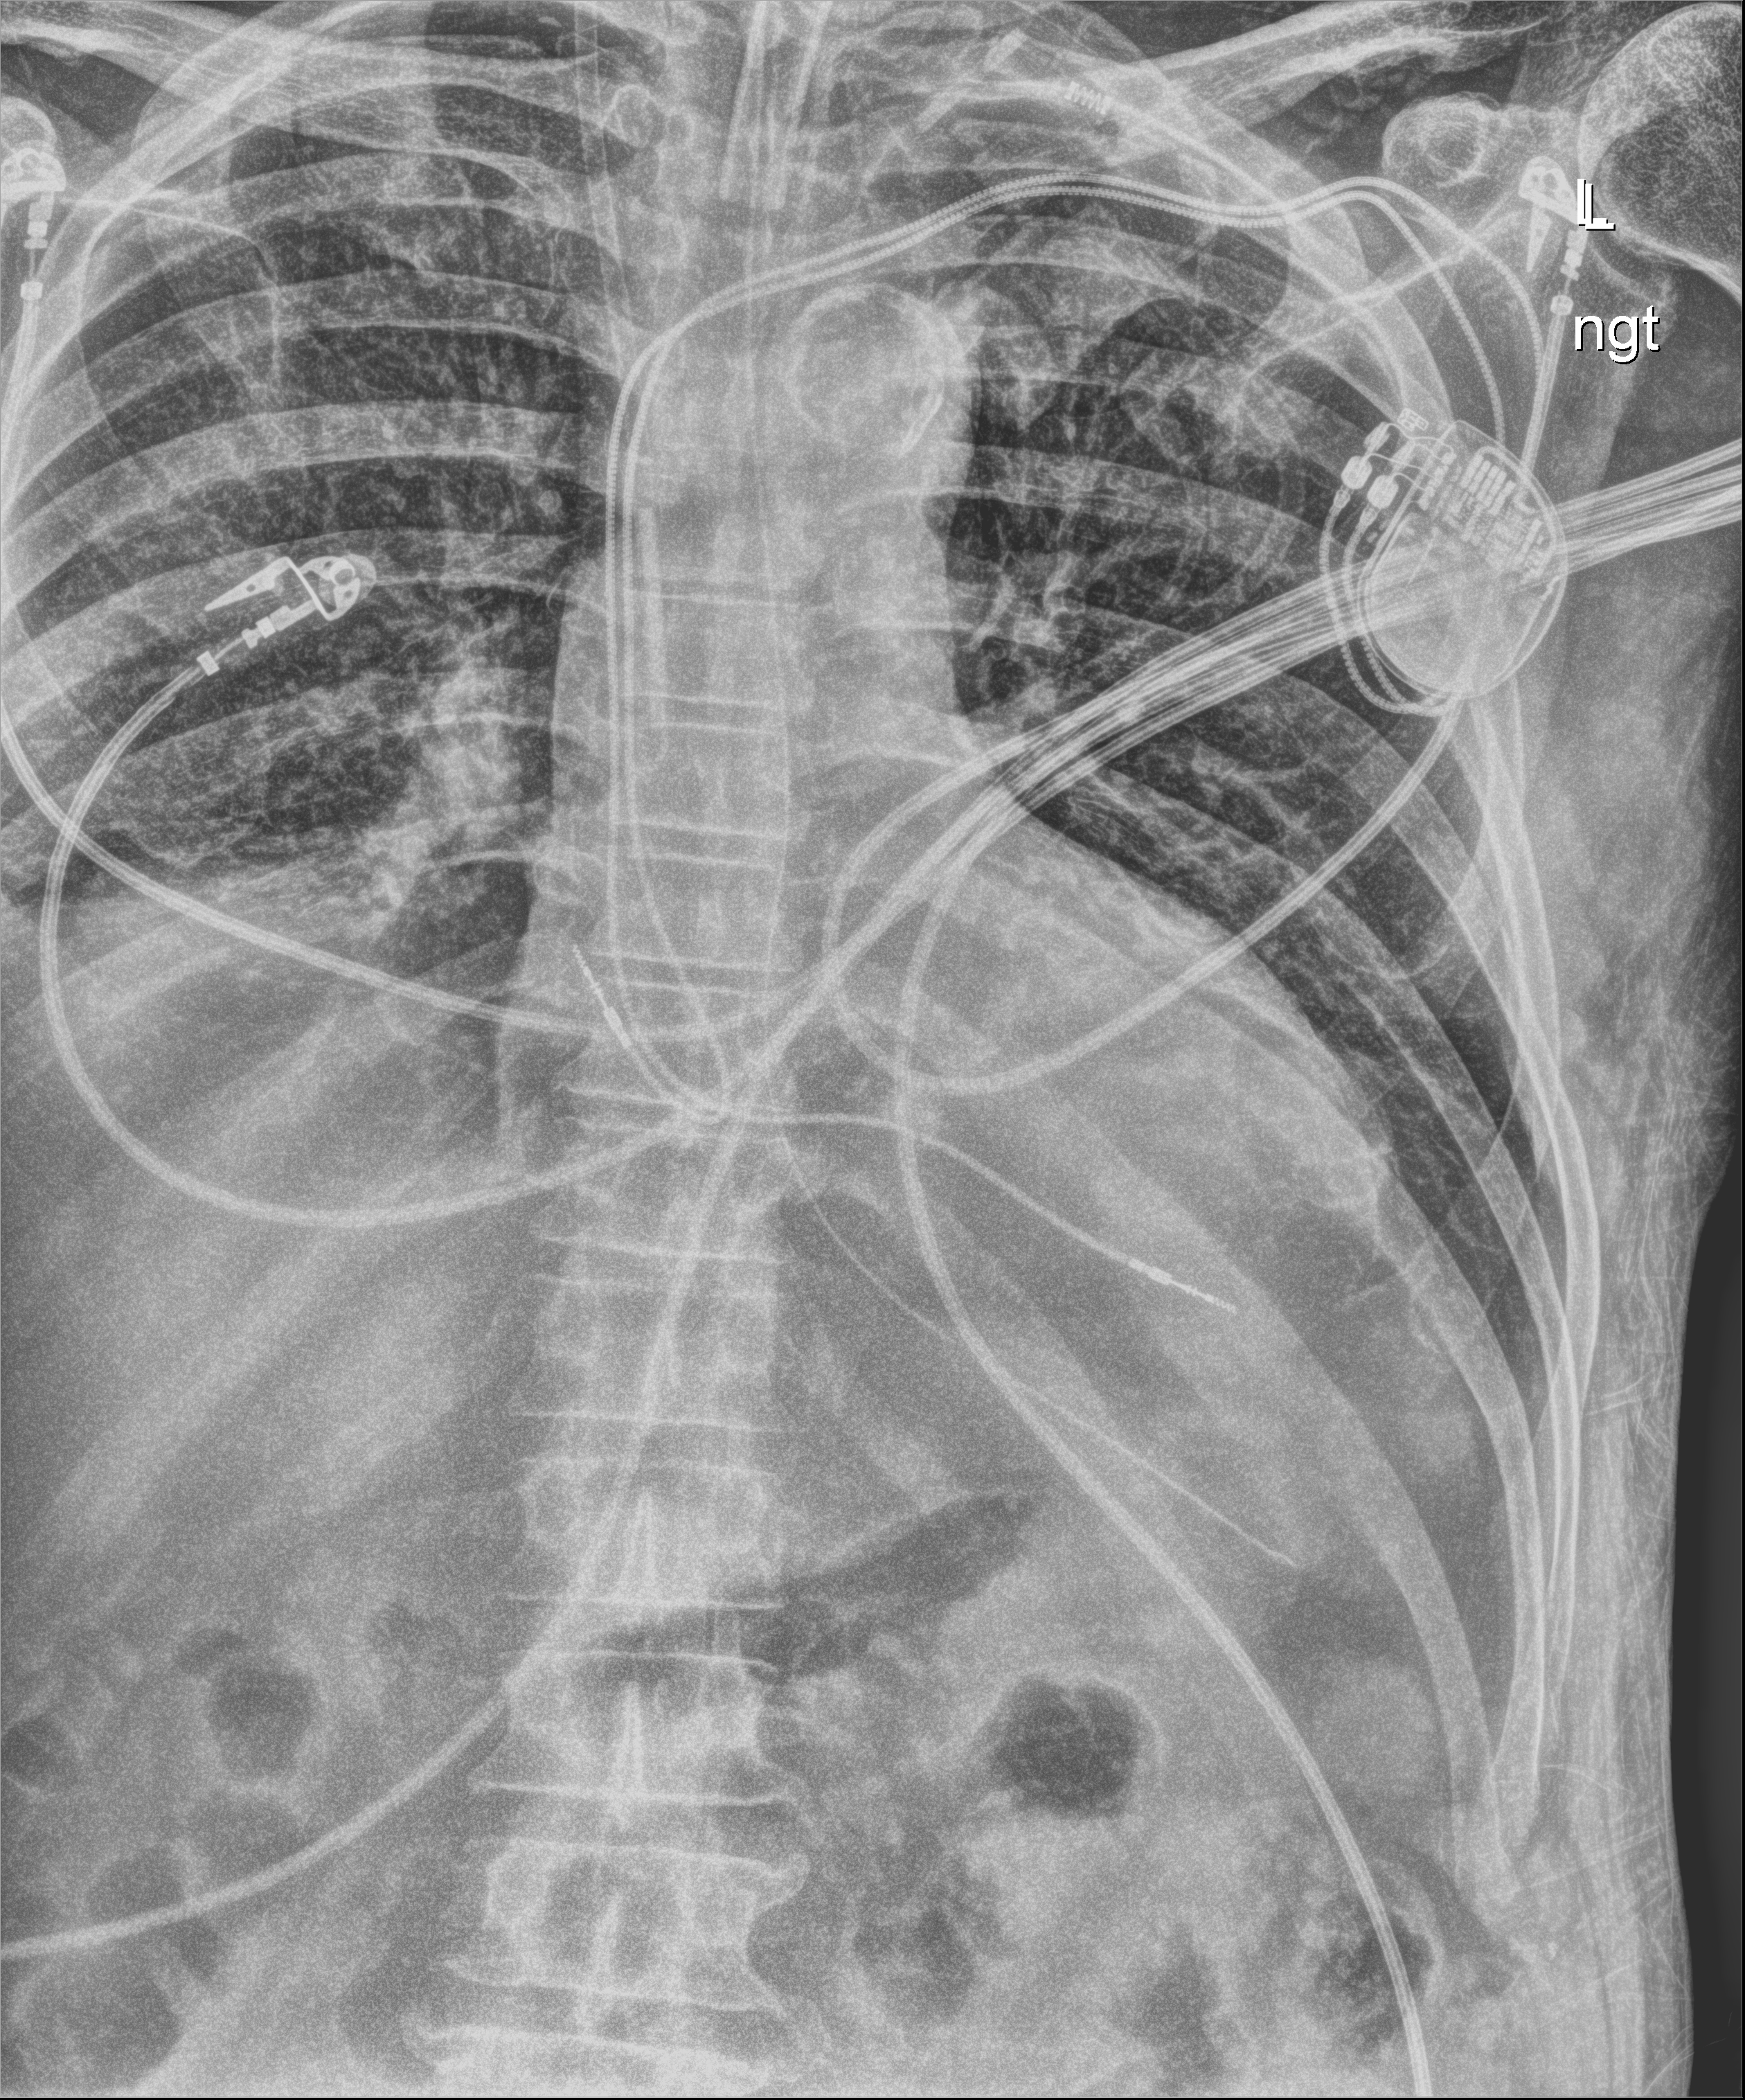
Chest radiograph; anteroposterior (AP) projection. Patient hospitalised with COVID-19; male, aged 60–74 years.
Hospital-stay facts (about this admission, not read from this image; timing relative to this image not recorded): mechanically ventilated during this hospital stay: yes; length of hospital stay: 41 days; admitted to intensive care during this hospital stay: yes.